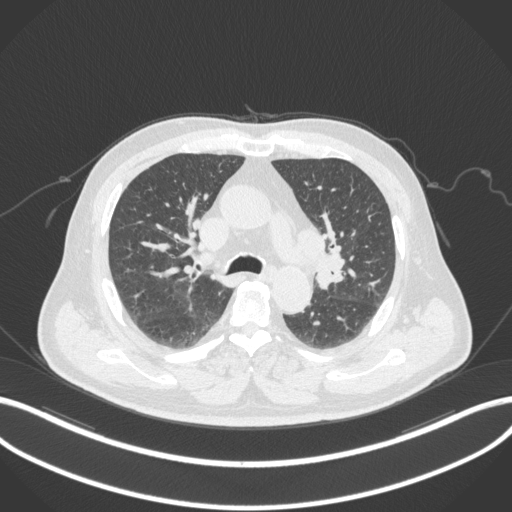
Chest CT, one axial slice. Slice 193 of 286 in the series (ordered by position). Reconstruction kernel B31f. 120 kVp. Lung window (W 1500 / L -600 HU). 1 mm slice thickness. 512 × 512 image matrix, field of view 400 × 400 mm. Patient: male, 67 years. Case-level facts recorded for this patient, not image findings: clinical TNM (as recorded): T2a N1 M0.
Annotated regions visible in this slice (rectangle marked by the reading radiologist):
- lung tumour (recorded histology: adenocarcinoma): box from (x=312, y=250) to (x=345, y=291) px